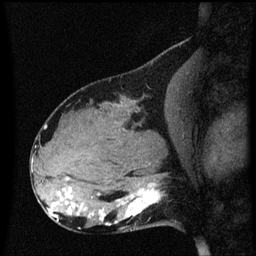
Breast MRI (dynamic contrast-enhanced), one sagittal slice; slice 27 of 60 in the series (ordered by position); dynamic contrast-enhanced series, image 2 of 3 at this slice position (ordered by acquisition); 1.5 T; TE 4.2 ms, TR 8.4 ms; 256 × 256 image matrix. Patient: female, 31 years. Case-level facts recorded for this patient, not image findings: setting: breast cancer imaged before/during neoadjuvant chemotherapy; receptor status: HR-positive, HER2-negative.
Structures marked on this image (semi-automatic segmentation, software-assisted and operator-edited):
- analysis volume of interest (the breast-tissue region the enhancement analysis was run in; not a lesion): bounding box (x1, y1, x2, y2) in pixels: (102, 166, 176, 229)
- tumour enhancement mask (voxels above the 70 % enhancement threshold inside the analysis volume of interest): (102, 184, 161, 225)